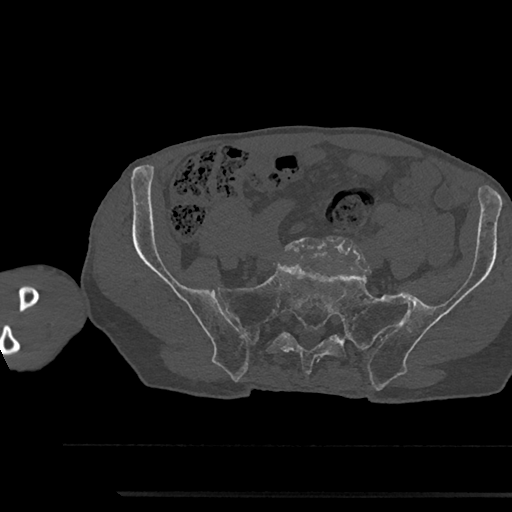
CT including the spine, one axial slice; slice 288 of 797 in the series (ordered by position); reconstruction kernel Br40s/3; 120 kVp; bone window (W 1800 / L 400 HU); 0.5 mm slice thickness; 512 × 512 image matrix. Patient: male, 79 years. Case-level facts recorded for this patient, not image findings: primary cancer: prostate.
Structures marked on this image (semi-automatic segmentation, software-assisted and operator-edited):
- L5 vertebra: bounding box [x1, y1, x2, y2] px = [284, 238, 358, 265]